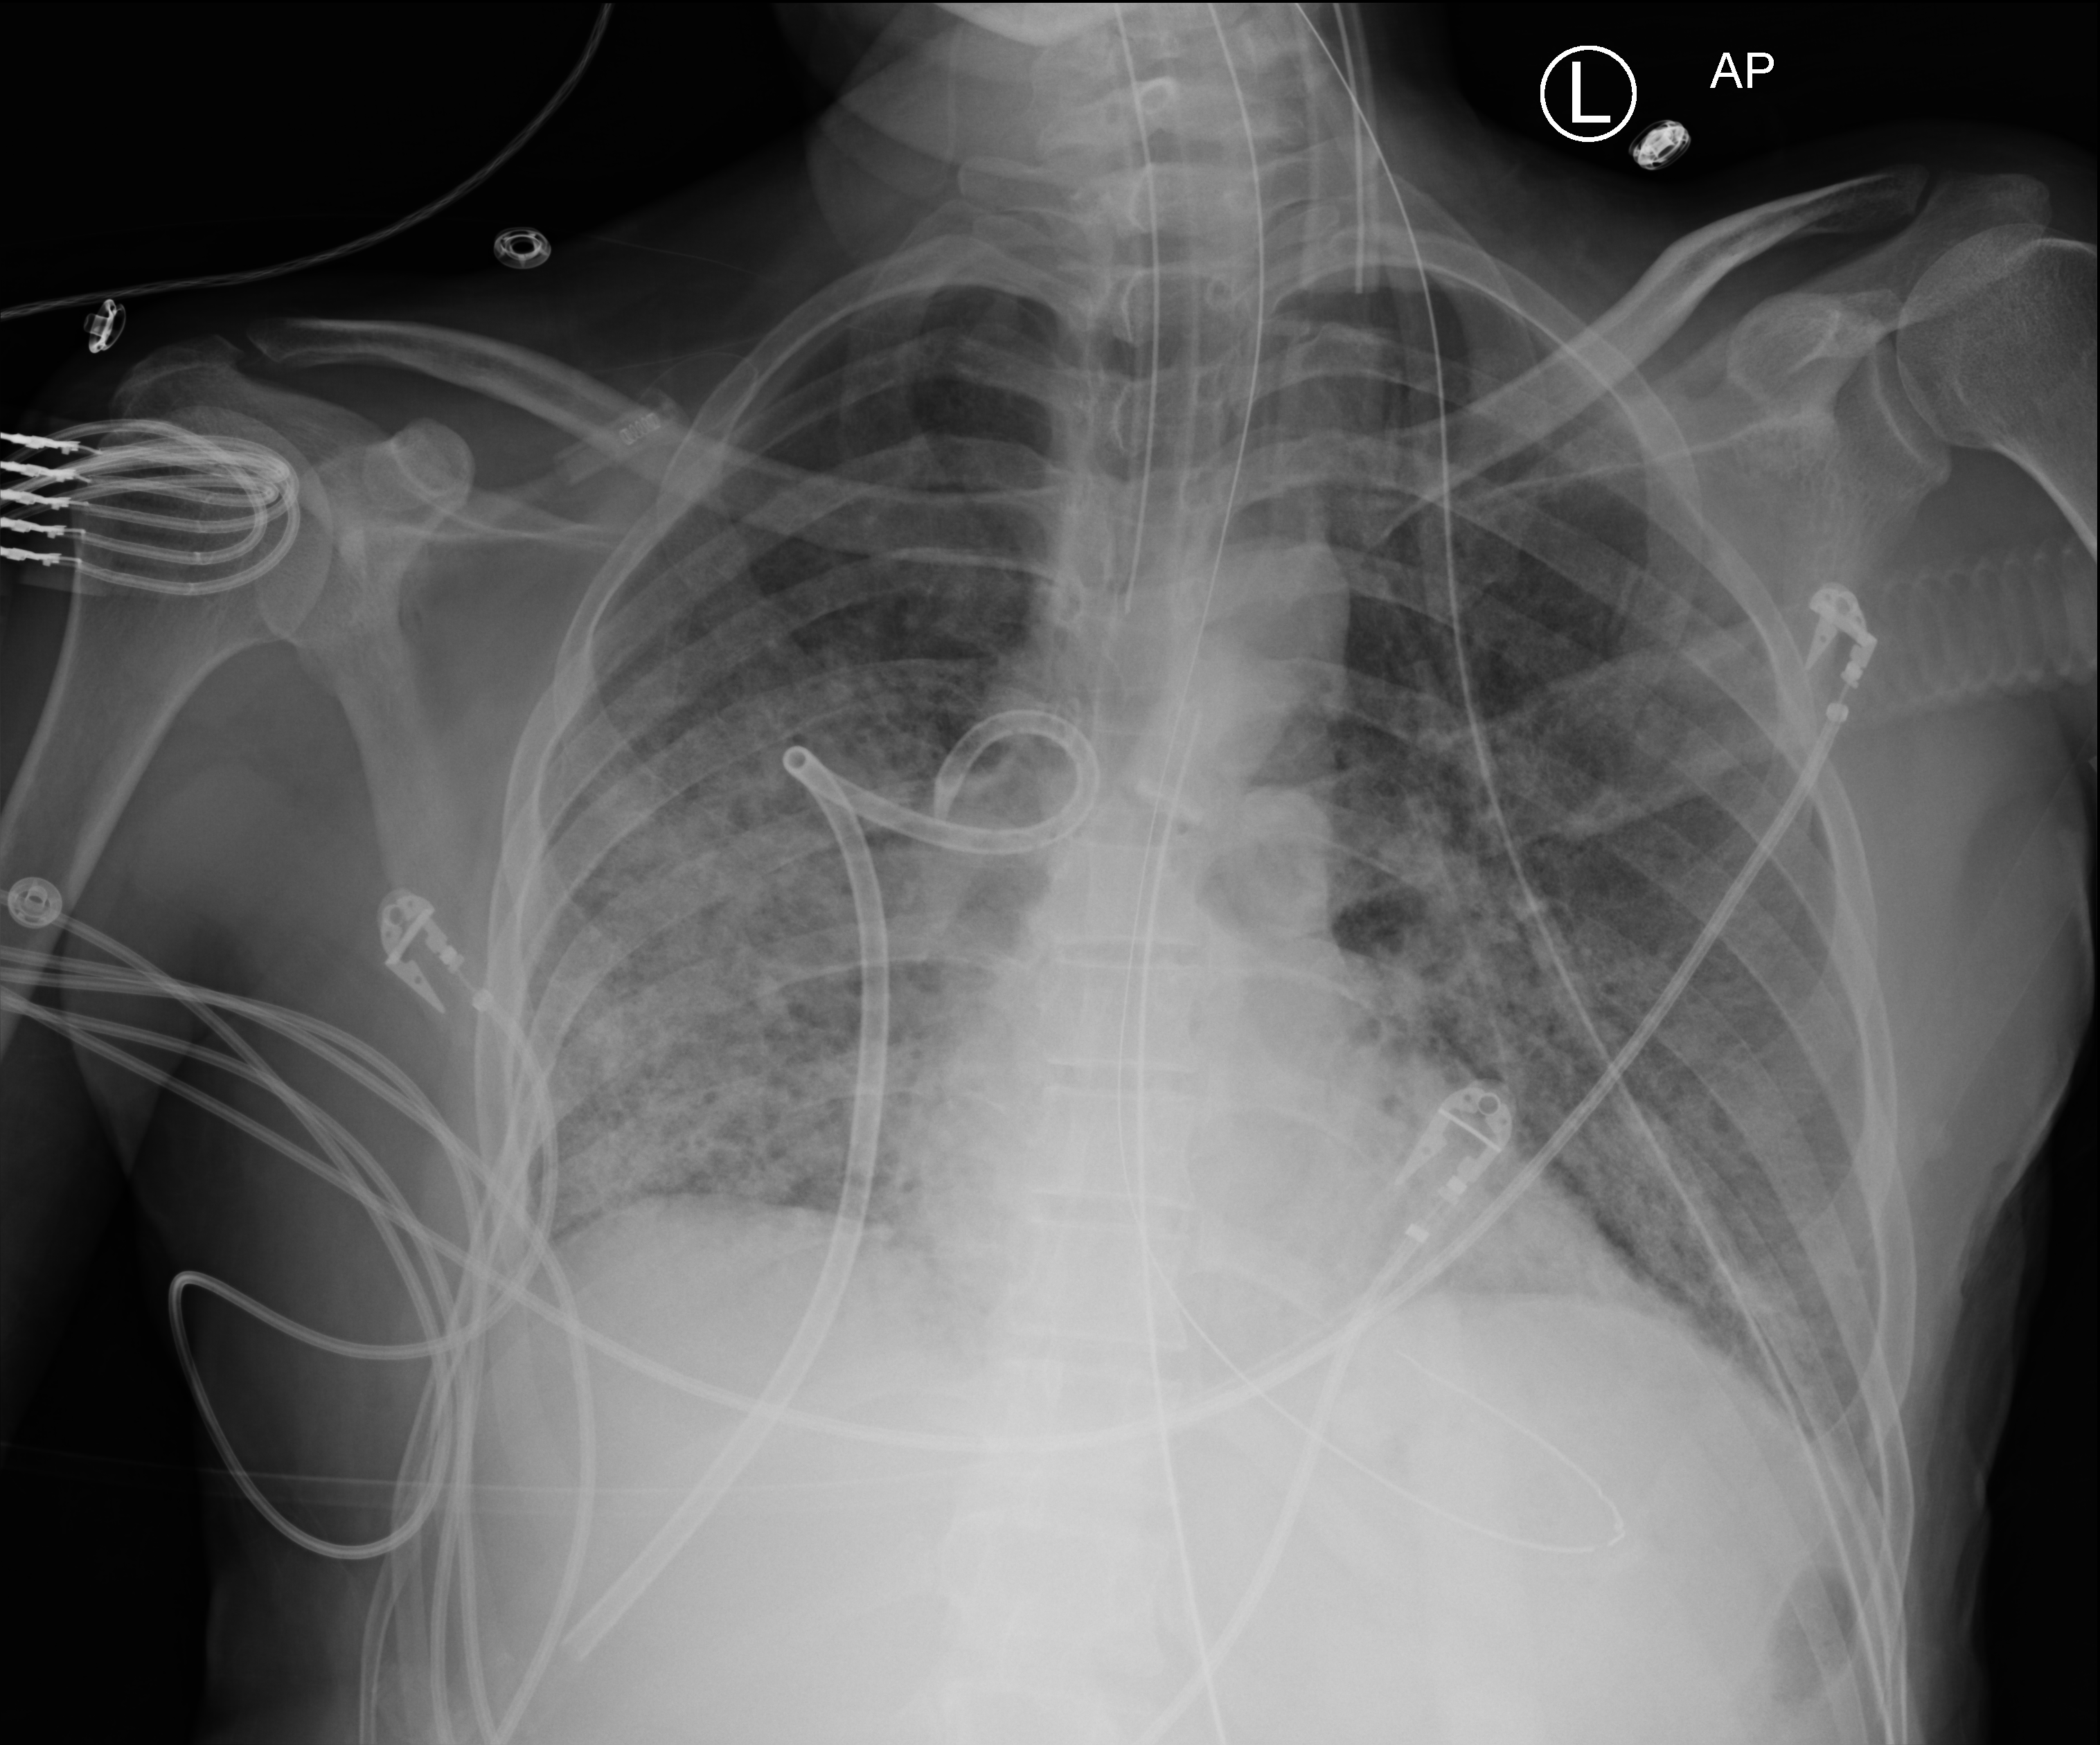
Bedside chest radiograph (computed radiography). Adult patient hospitalised with COVID-19, age 18–59 years.
Admission-level facts for this patient (not findings on this image; timing relative to this image not recorded): mechanically ventilated during this hospital stay: yes; admitted to intensive care during this hospital stay: yes; other chronic lung disease (admission record): no.